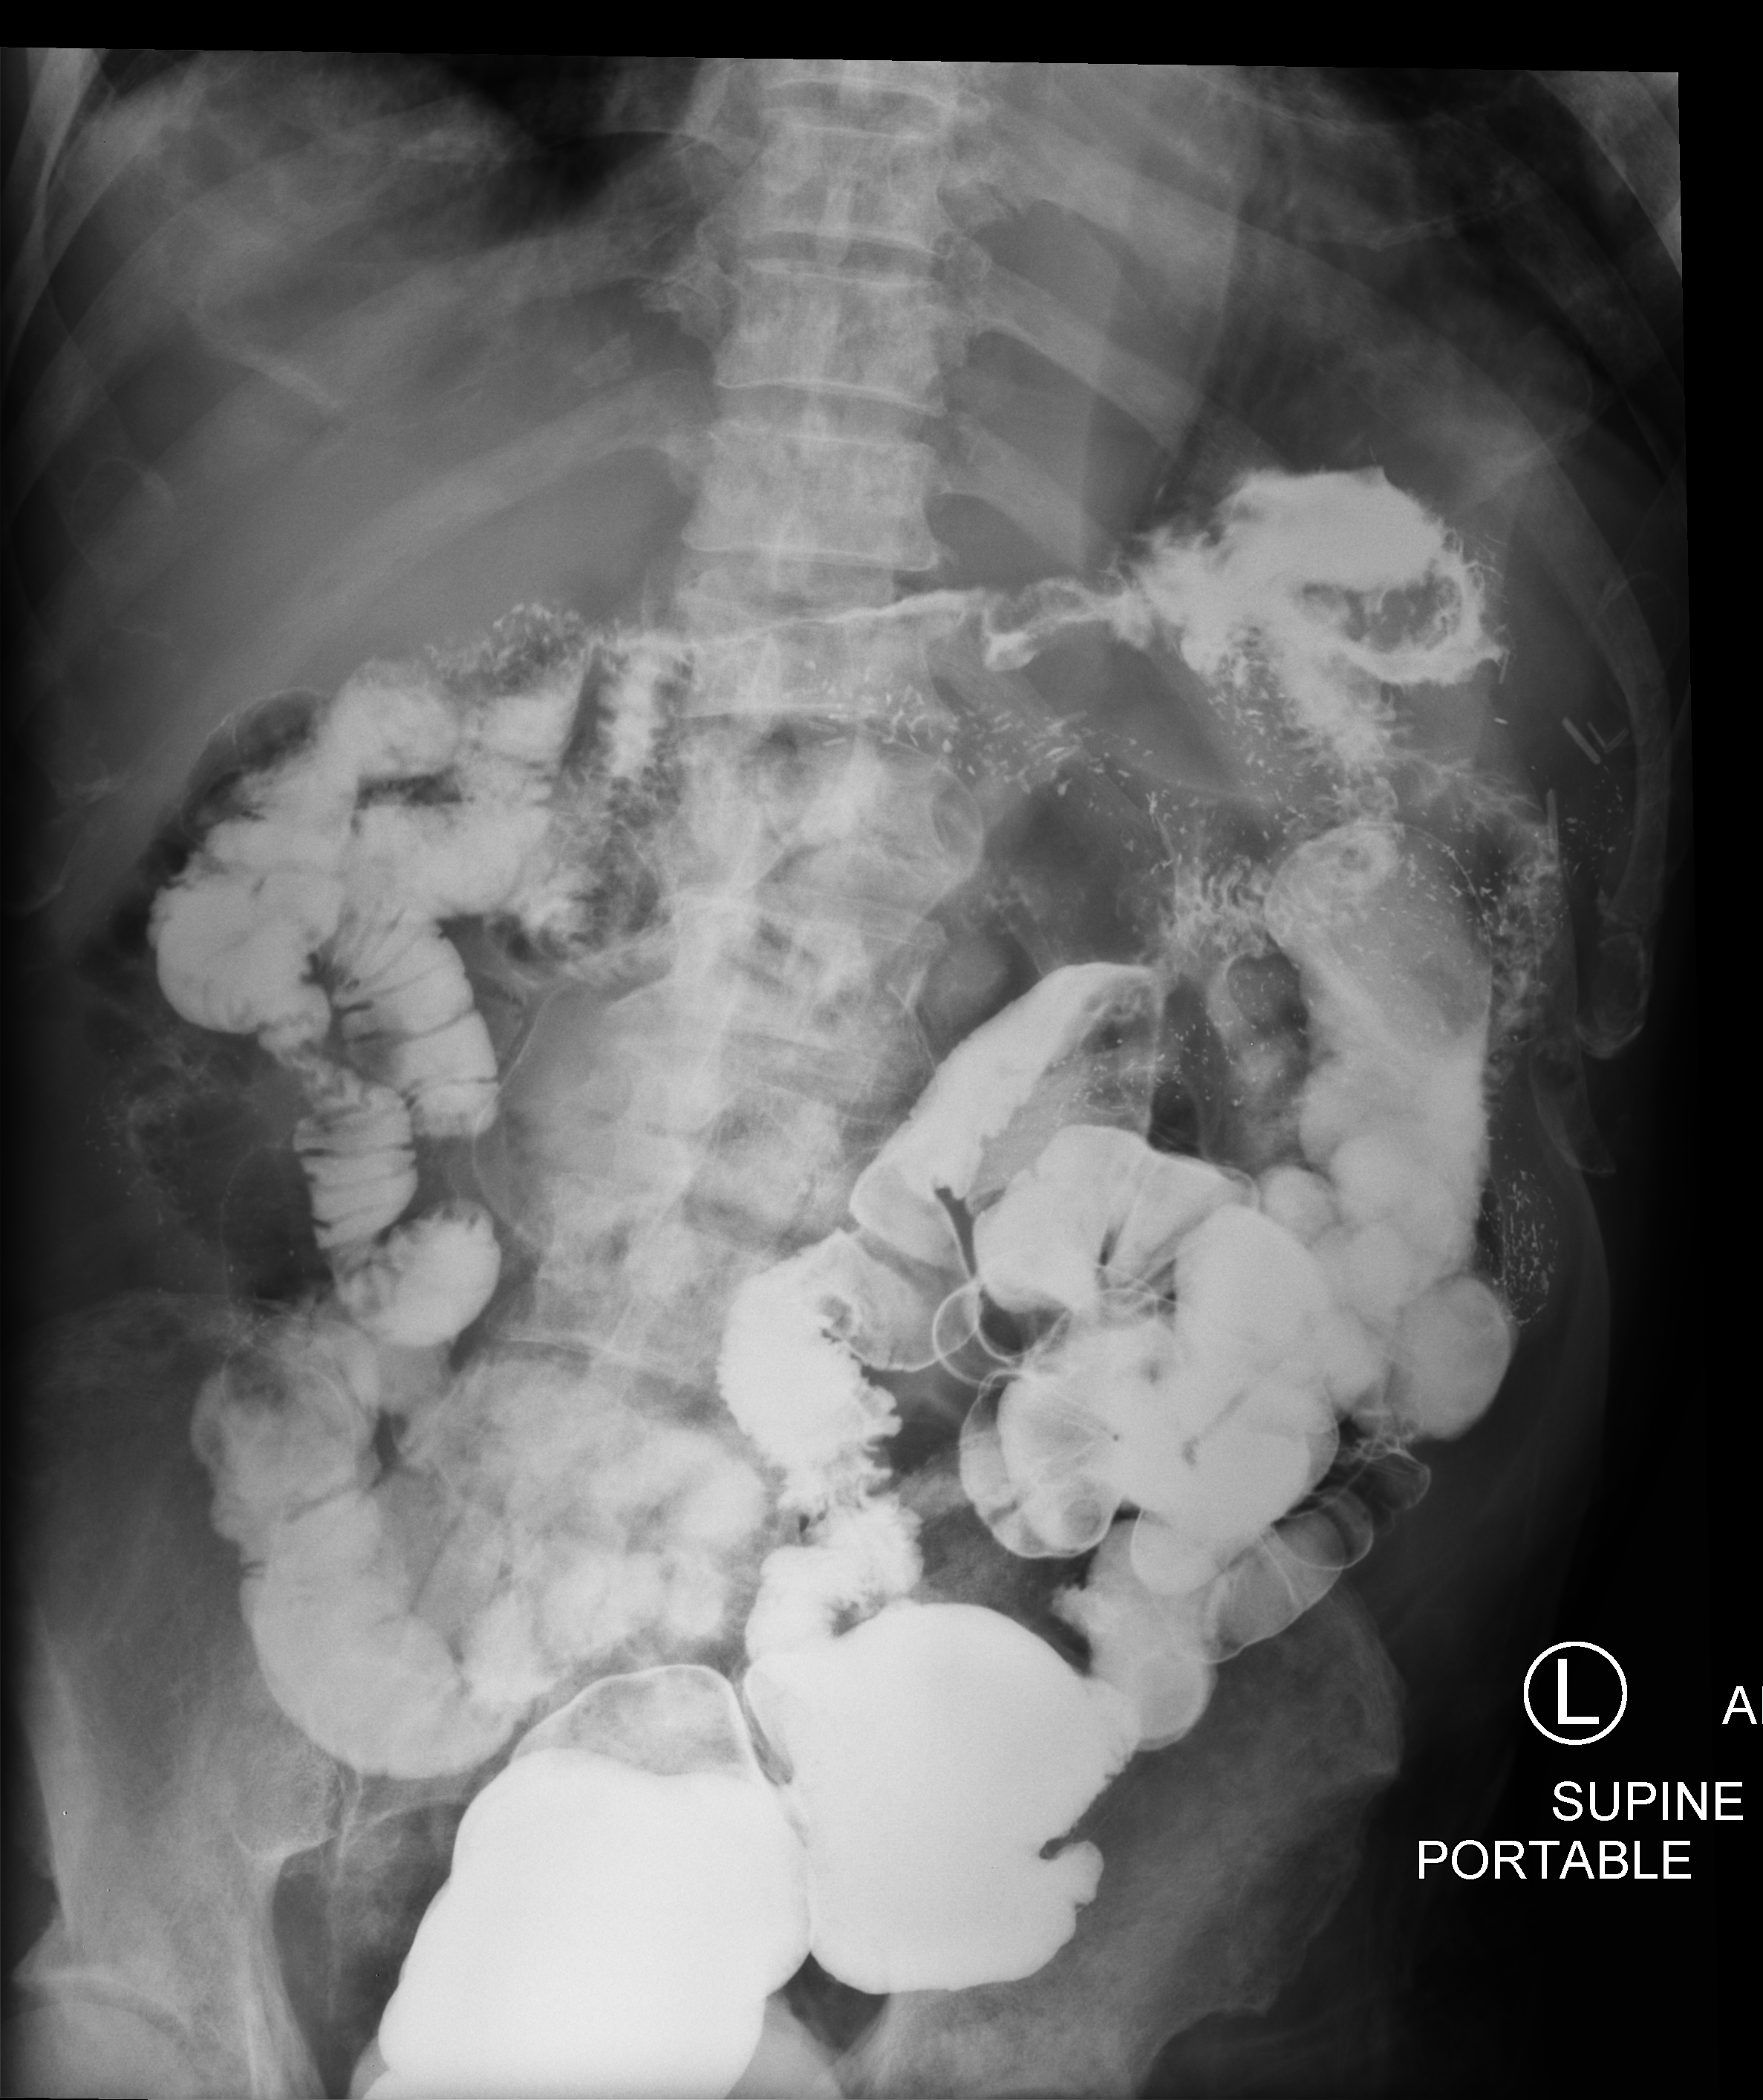
Portable abdomen radiograph, anteroposterior (AP) projection. Male patient hospitalised with COVID-19, age 75–90 years.
Hospital-stay facts (about this admission, not read from this image; timing relative to this image not recorded): length of hospital stay: 12 days; mechanically ventilated during this hospital stay: no.